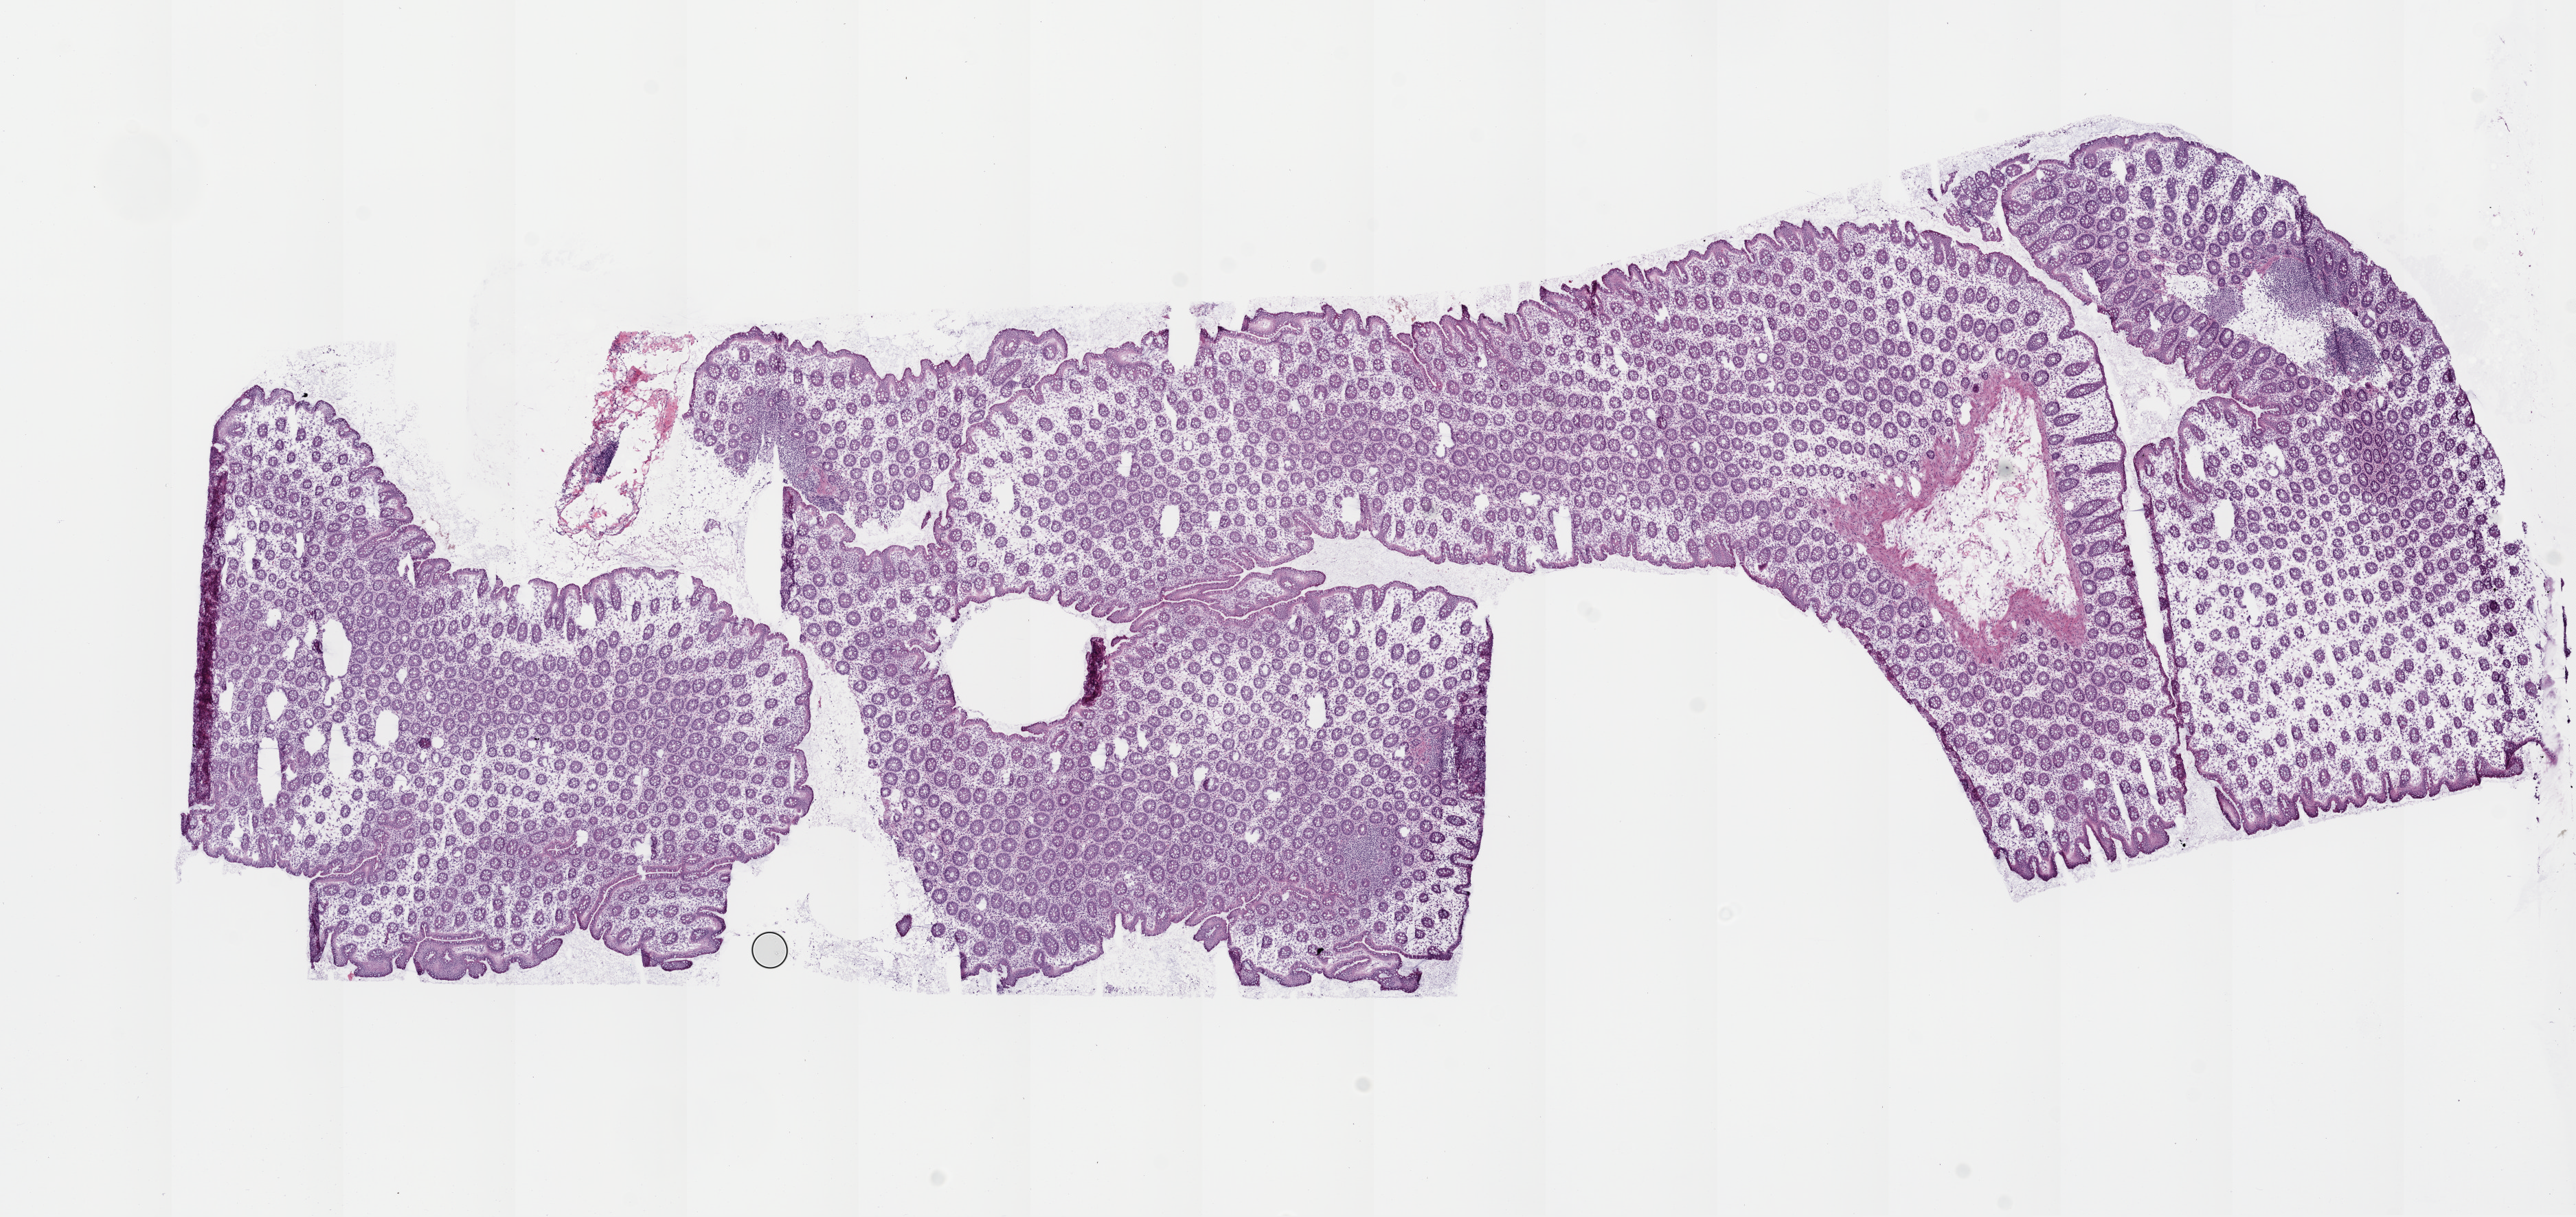
Whole-slide histology image, H&E — whole scanned area (about 15.0 x 7.1 mm) shown as a low-resolution overview; frozen section from the top of the tissue portion; colon, solid tissue normal (non-tumour tissue) sample. Male, age 70 years at initial diagnosis.
This section: solid tissue normal sample (biorepository sample class). Patient diagnosis: Adenocarcinoma, NOS.